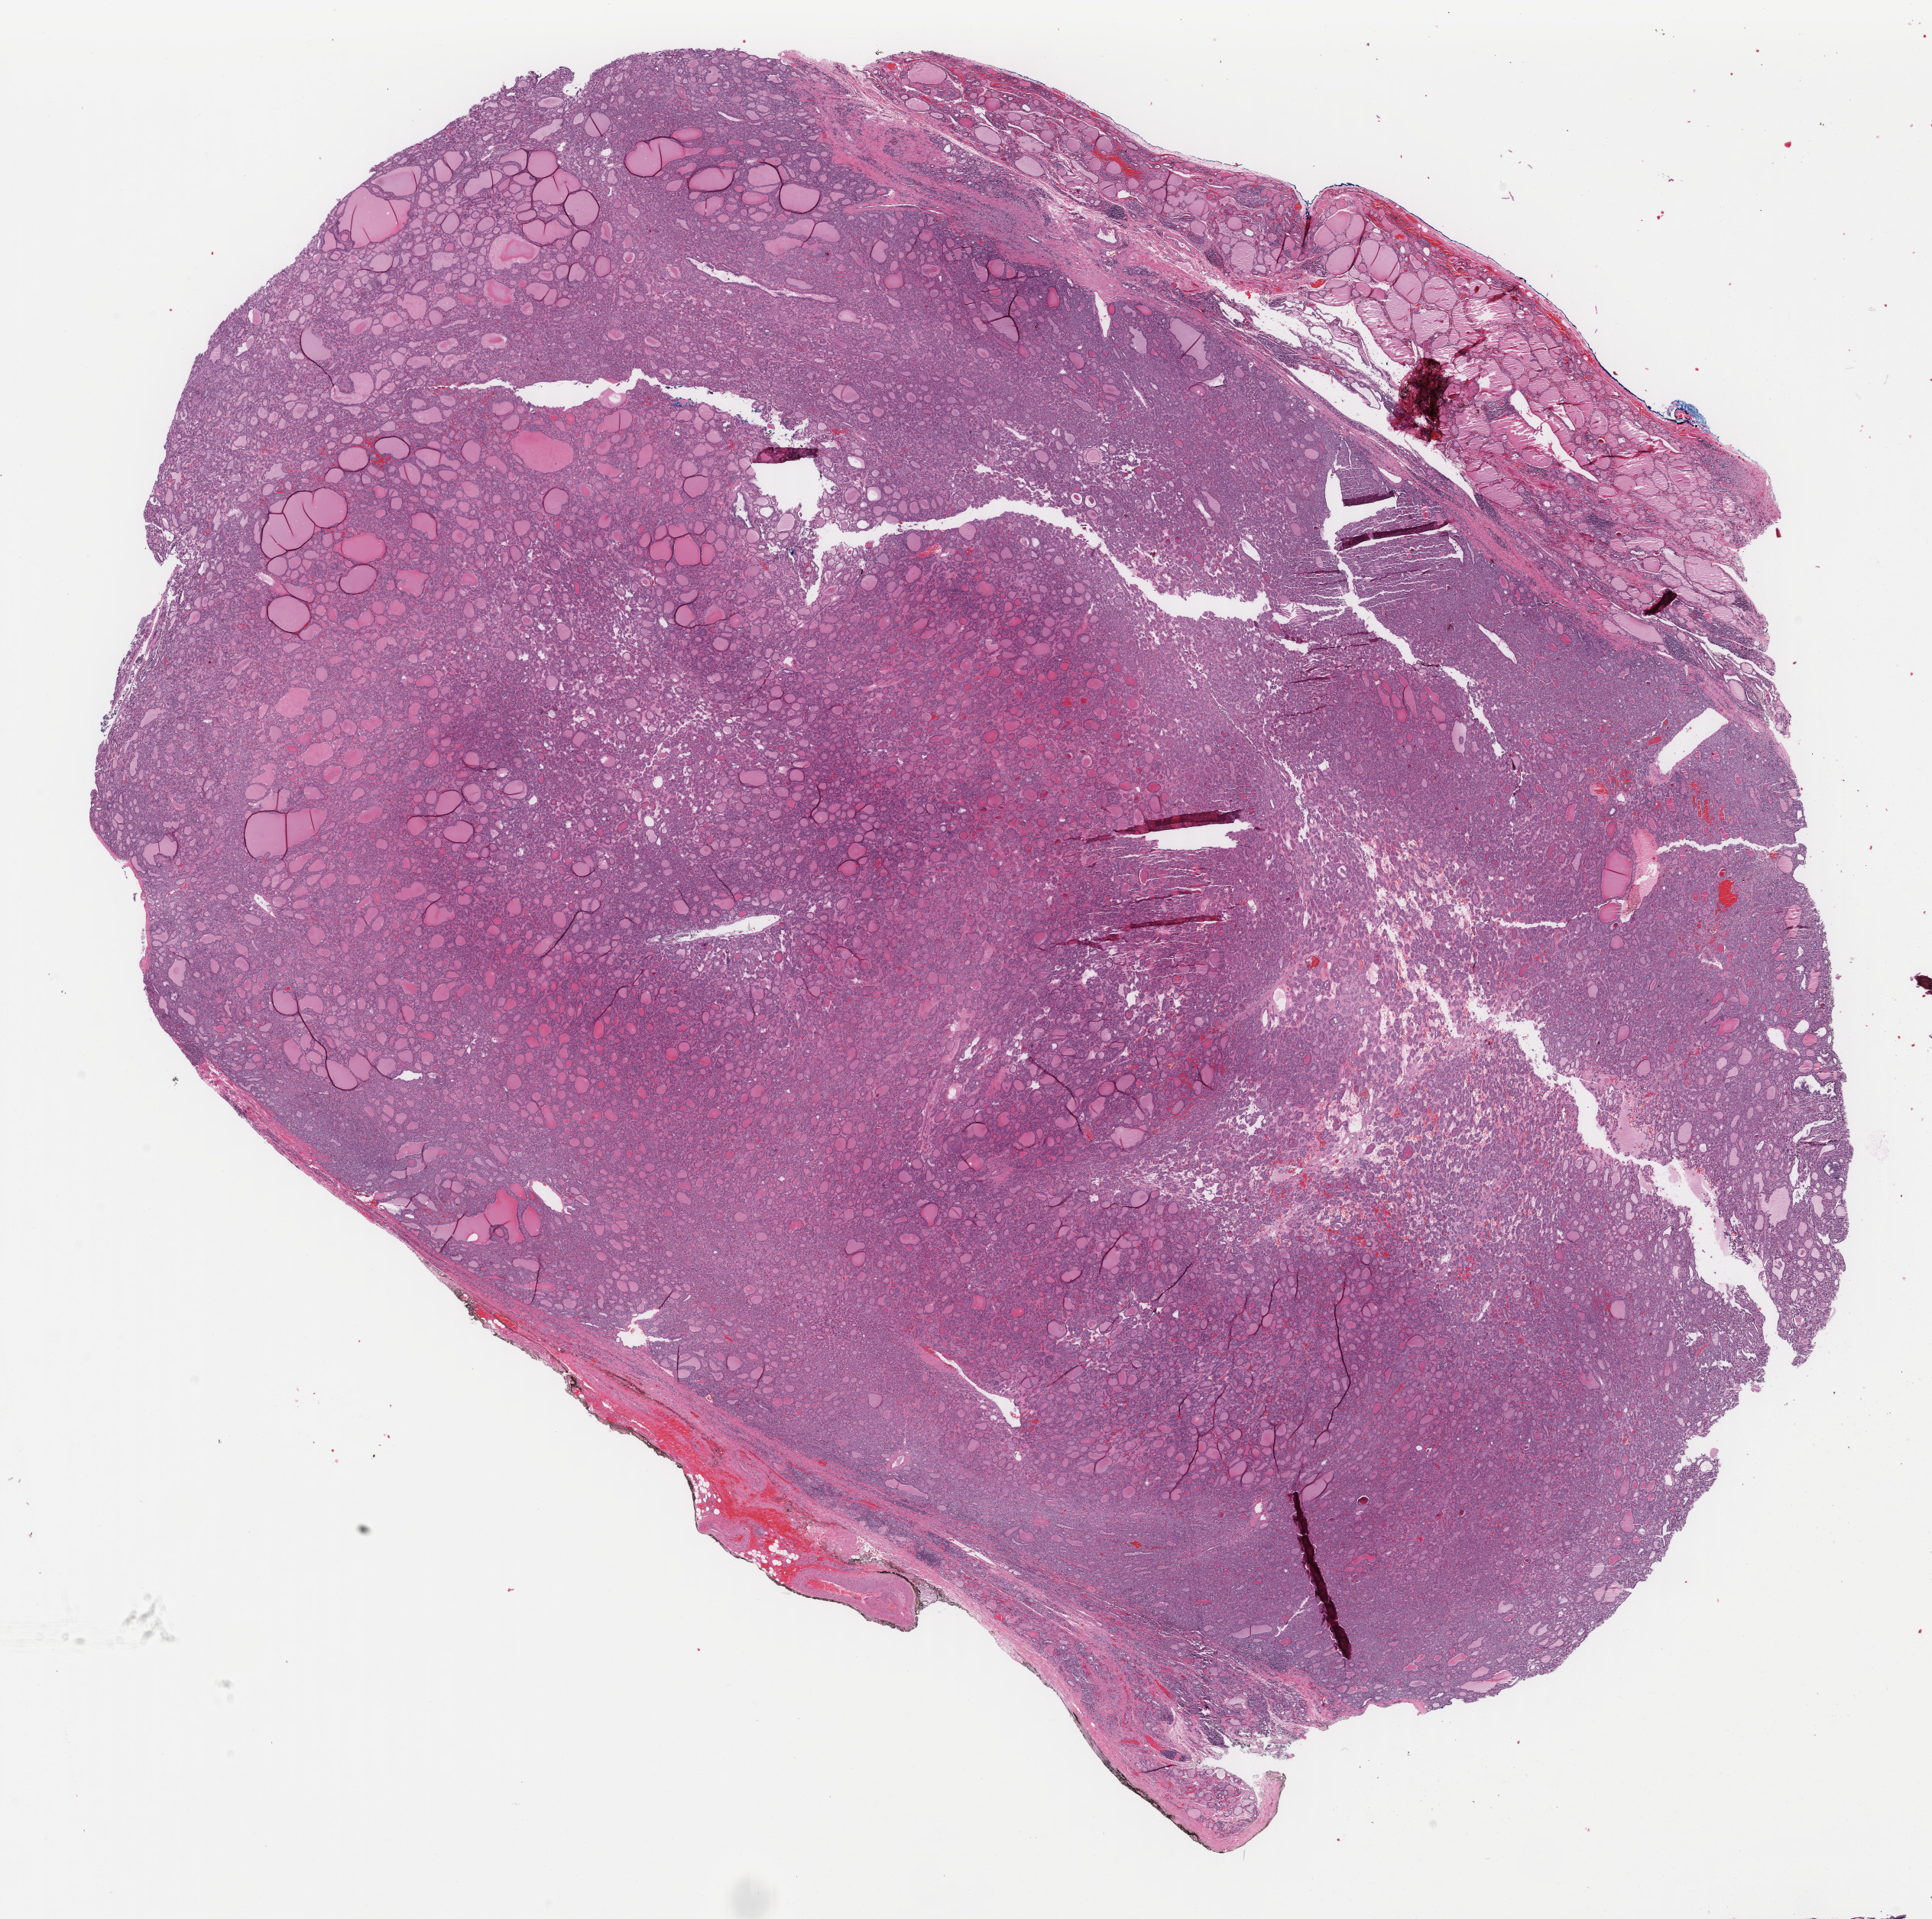
Digitized H&E-stained tissue section (whole slide) — a low-resolution overview of the entire scanned area, about 20.1 x 19.9 mm (from a 40x scan), formalin-fixed paraffin-embedded (FFPE) diagnostic section, sample: primary tumour, thyroid. Patient: female, age at initial diagnosis 45 years.
AJCC pathologic stage: I. Histologic diagnosis: Papillary carcinoma, follicular variant (thyroid gland).